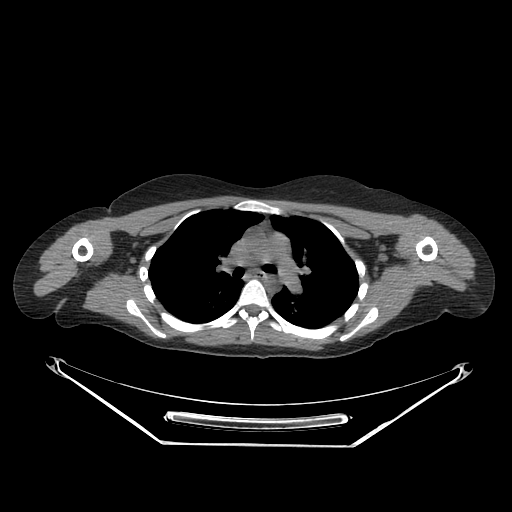
CT of an extremity soft-tissue mass (from a PET/CT study), one axial slice; slice 198 of 267 in the series (ordered by position); reconstruction kernel SOFT; soft-tissue window (W 400 / L 40 HU); 3.75 mm slice thickness; 512 × 512 image matrix. Female patient. From the clinical record (not read from this slice): histological type: malignant fibrous histiocytoma; grade: low; site of the primary tumour: left arm.
Annotated regions visible in this slice (expert contour drawn on MRI and transferred to this co-registered scan by the dataset authors):
- gross tumour volume (mass): bounding box <448,262,455,271> (left, top, right, bottom; pixels)